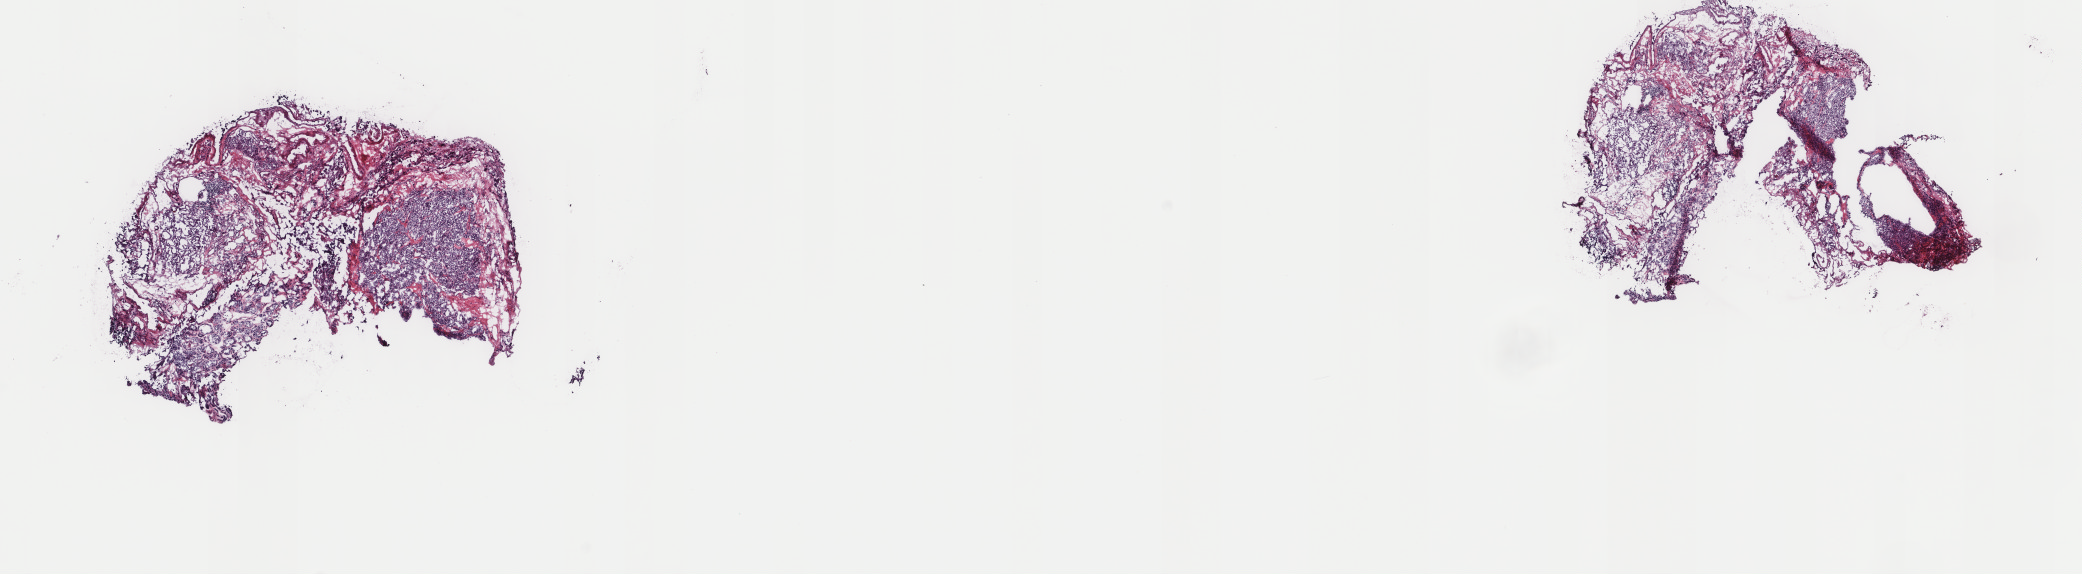
Whole-slide histology image, Hematoxylin and eosin (H&E) stained — low-resolution overview of the scanned area, about 16.5 x 4.6 mm (from a 40x scan), frozen section, sample: primary tumour, thyroid. Patient: female, age at initial diagnosis 71 years. Pathologist review of this section (percent, as recorded): tumour cells 80%, tumour nuclei 80%, normal cells 0%, stromal cells 20%, necrosis 0%. Inflammatory infiltration, as recorded: lymphocyte infiltration 1%, monocyte infiltration 0%, neutrophil infiltration 0%.
Diagnosis: Papillary carcinoma, follicular variant. Laterality: right. Lymph nodes positive (case pathology): 0 of 3 examined. AJCC pathologic stage: II (7th edition).